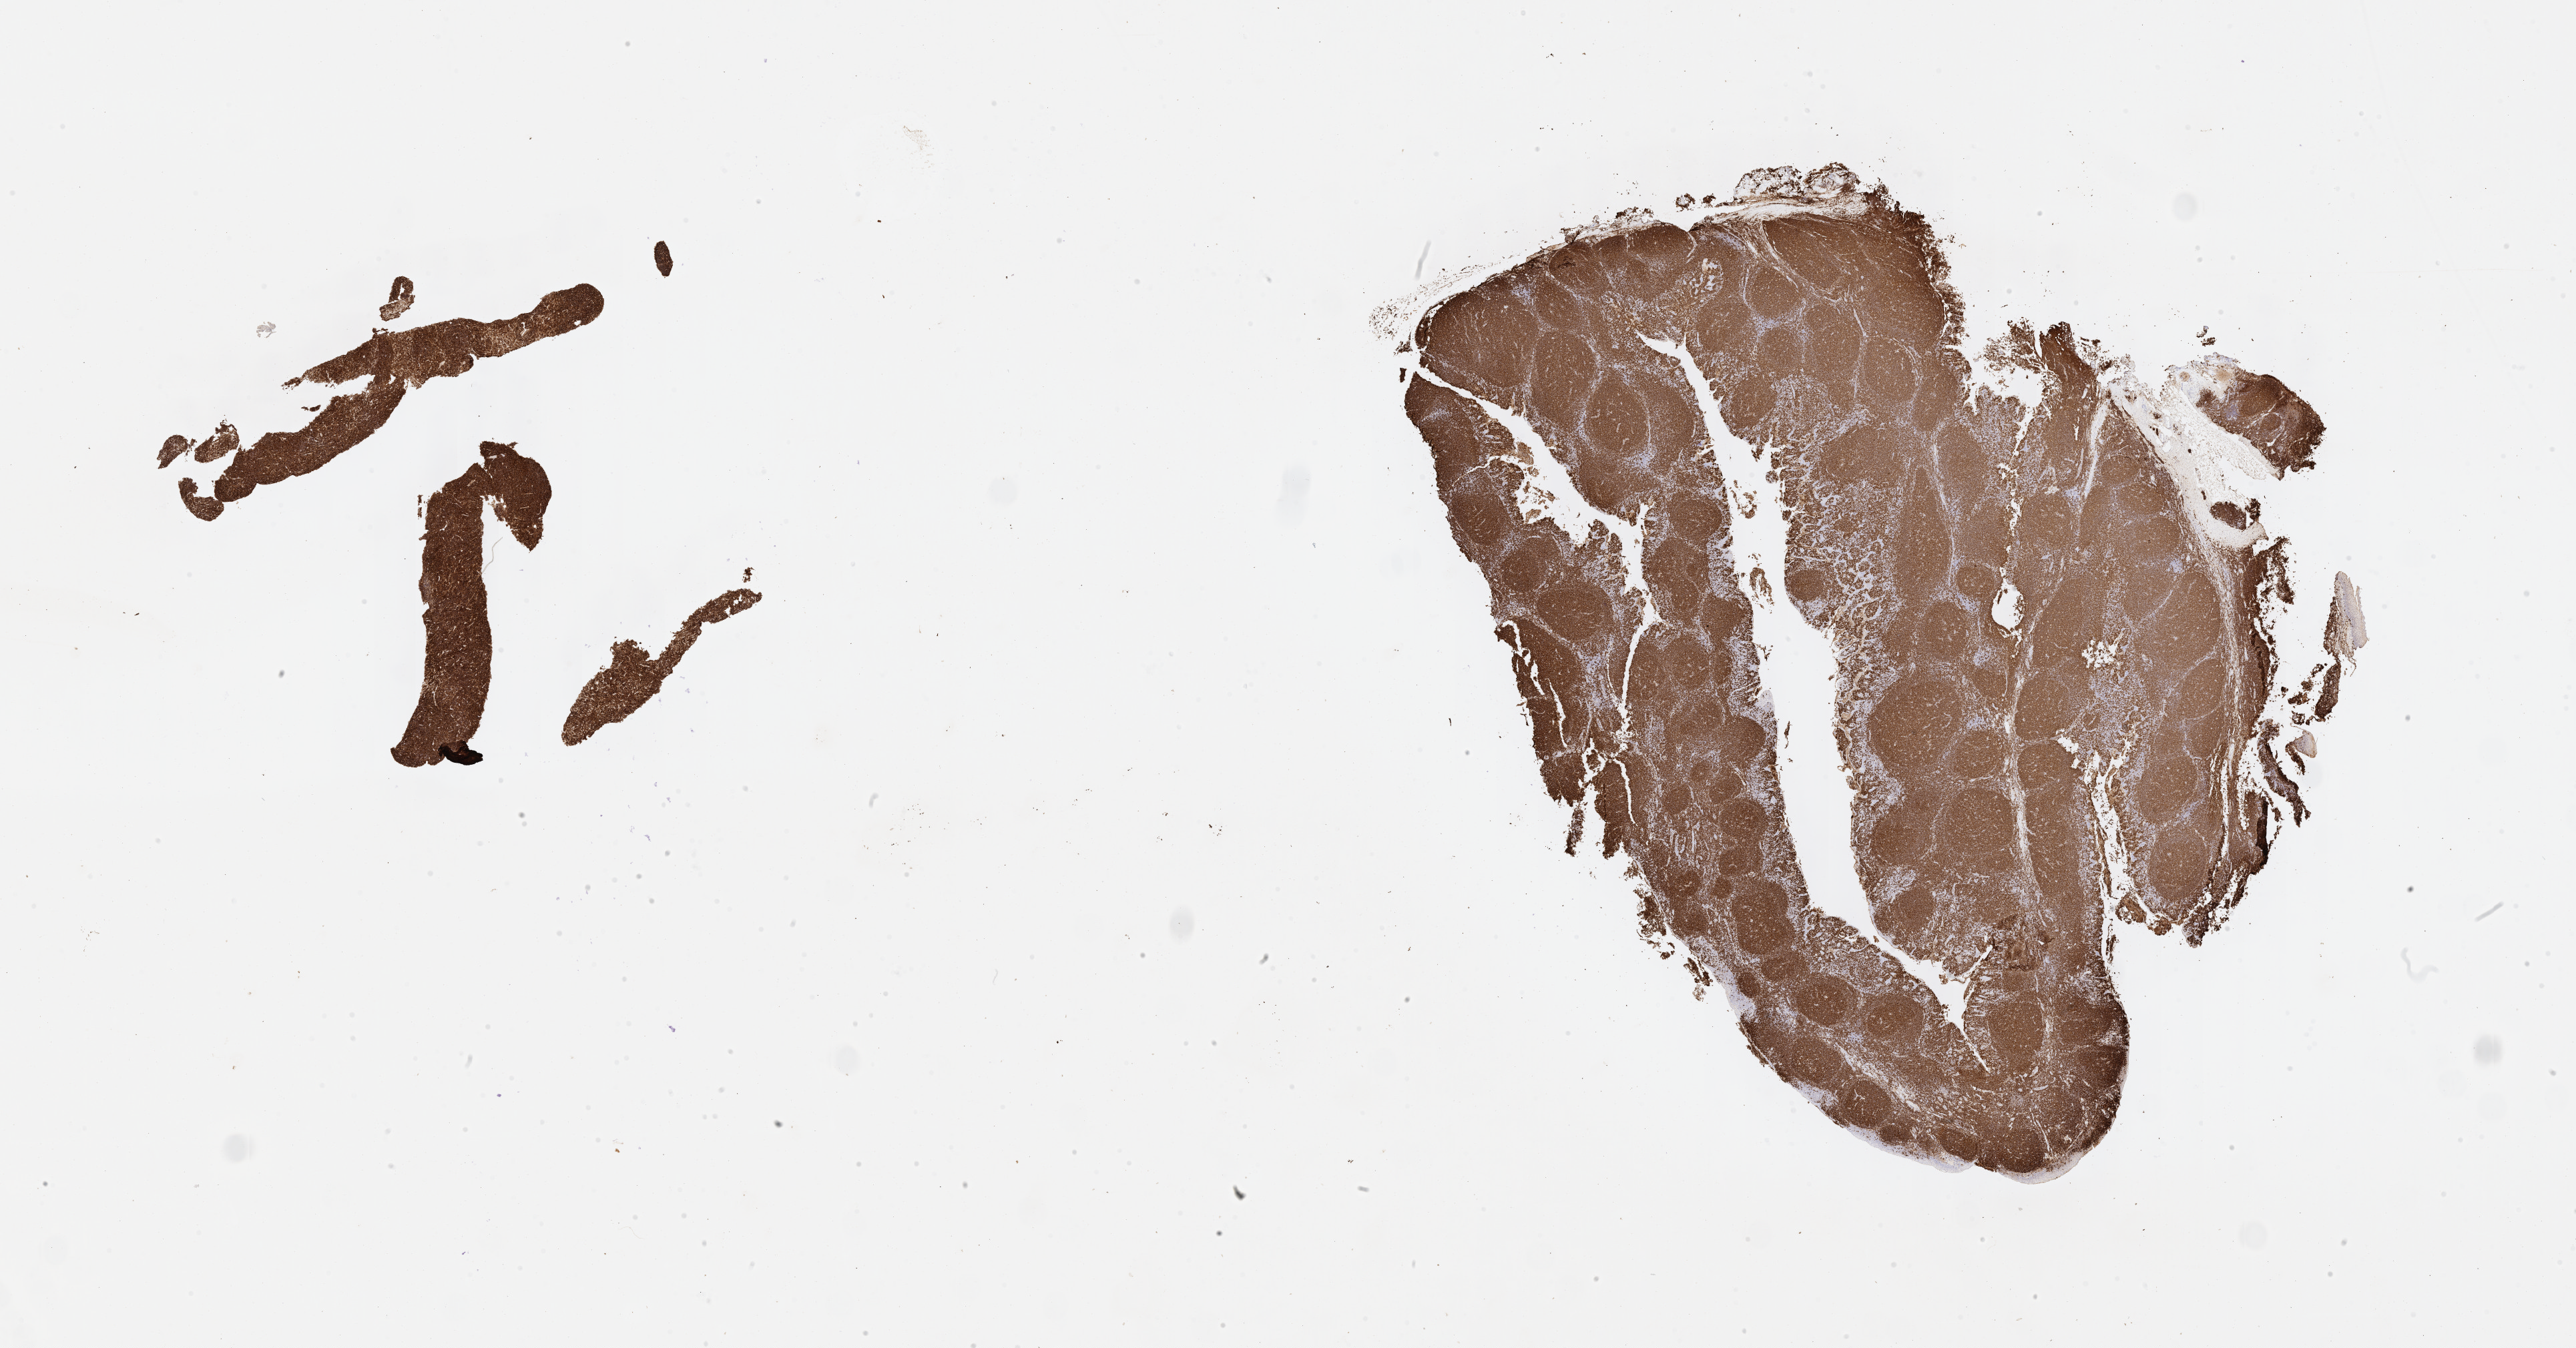
Immunohistochemistry (IHC) whole-slide image stained for CD20, low-resolution overview of the scanned area, about 31.2 x 16.3 mm; specimen: tumor tissue; site: abdomen proper. Male patient; age at initial diagnosis 2 years.
Histologic diagnosis: Diffuse large B-cell lymphoma, NOS.